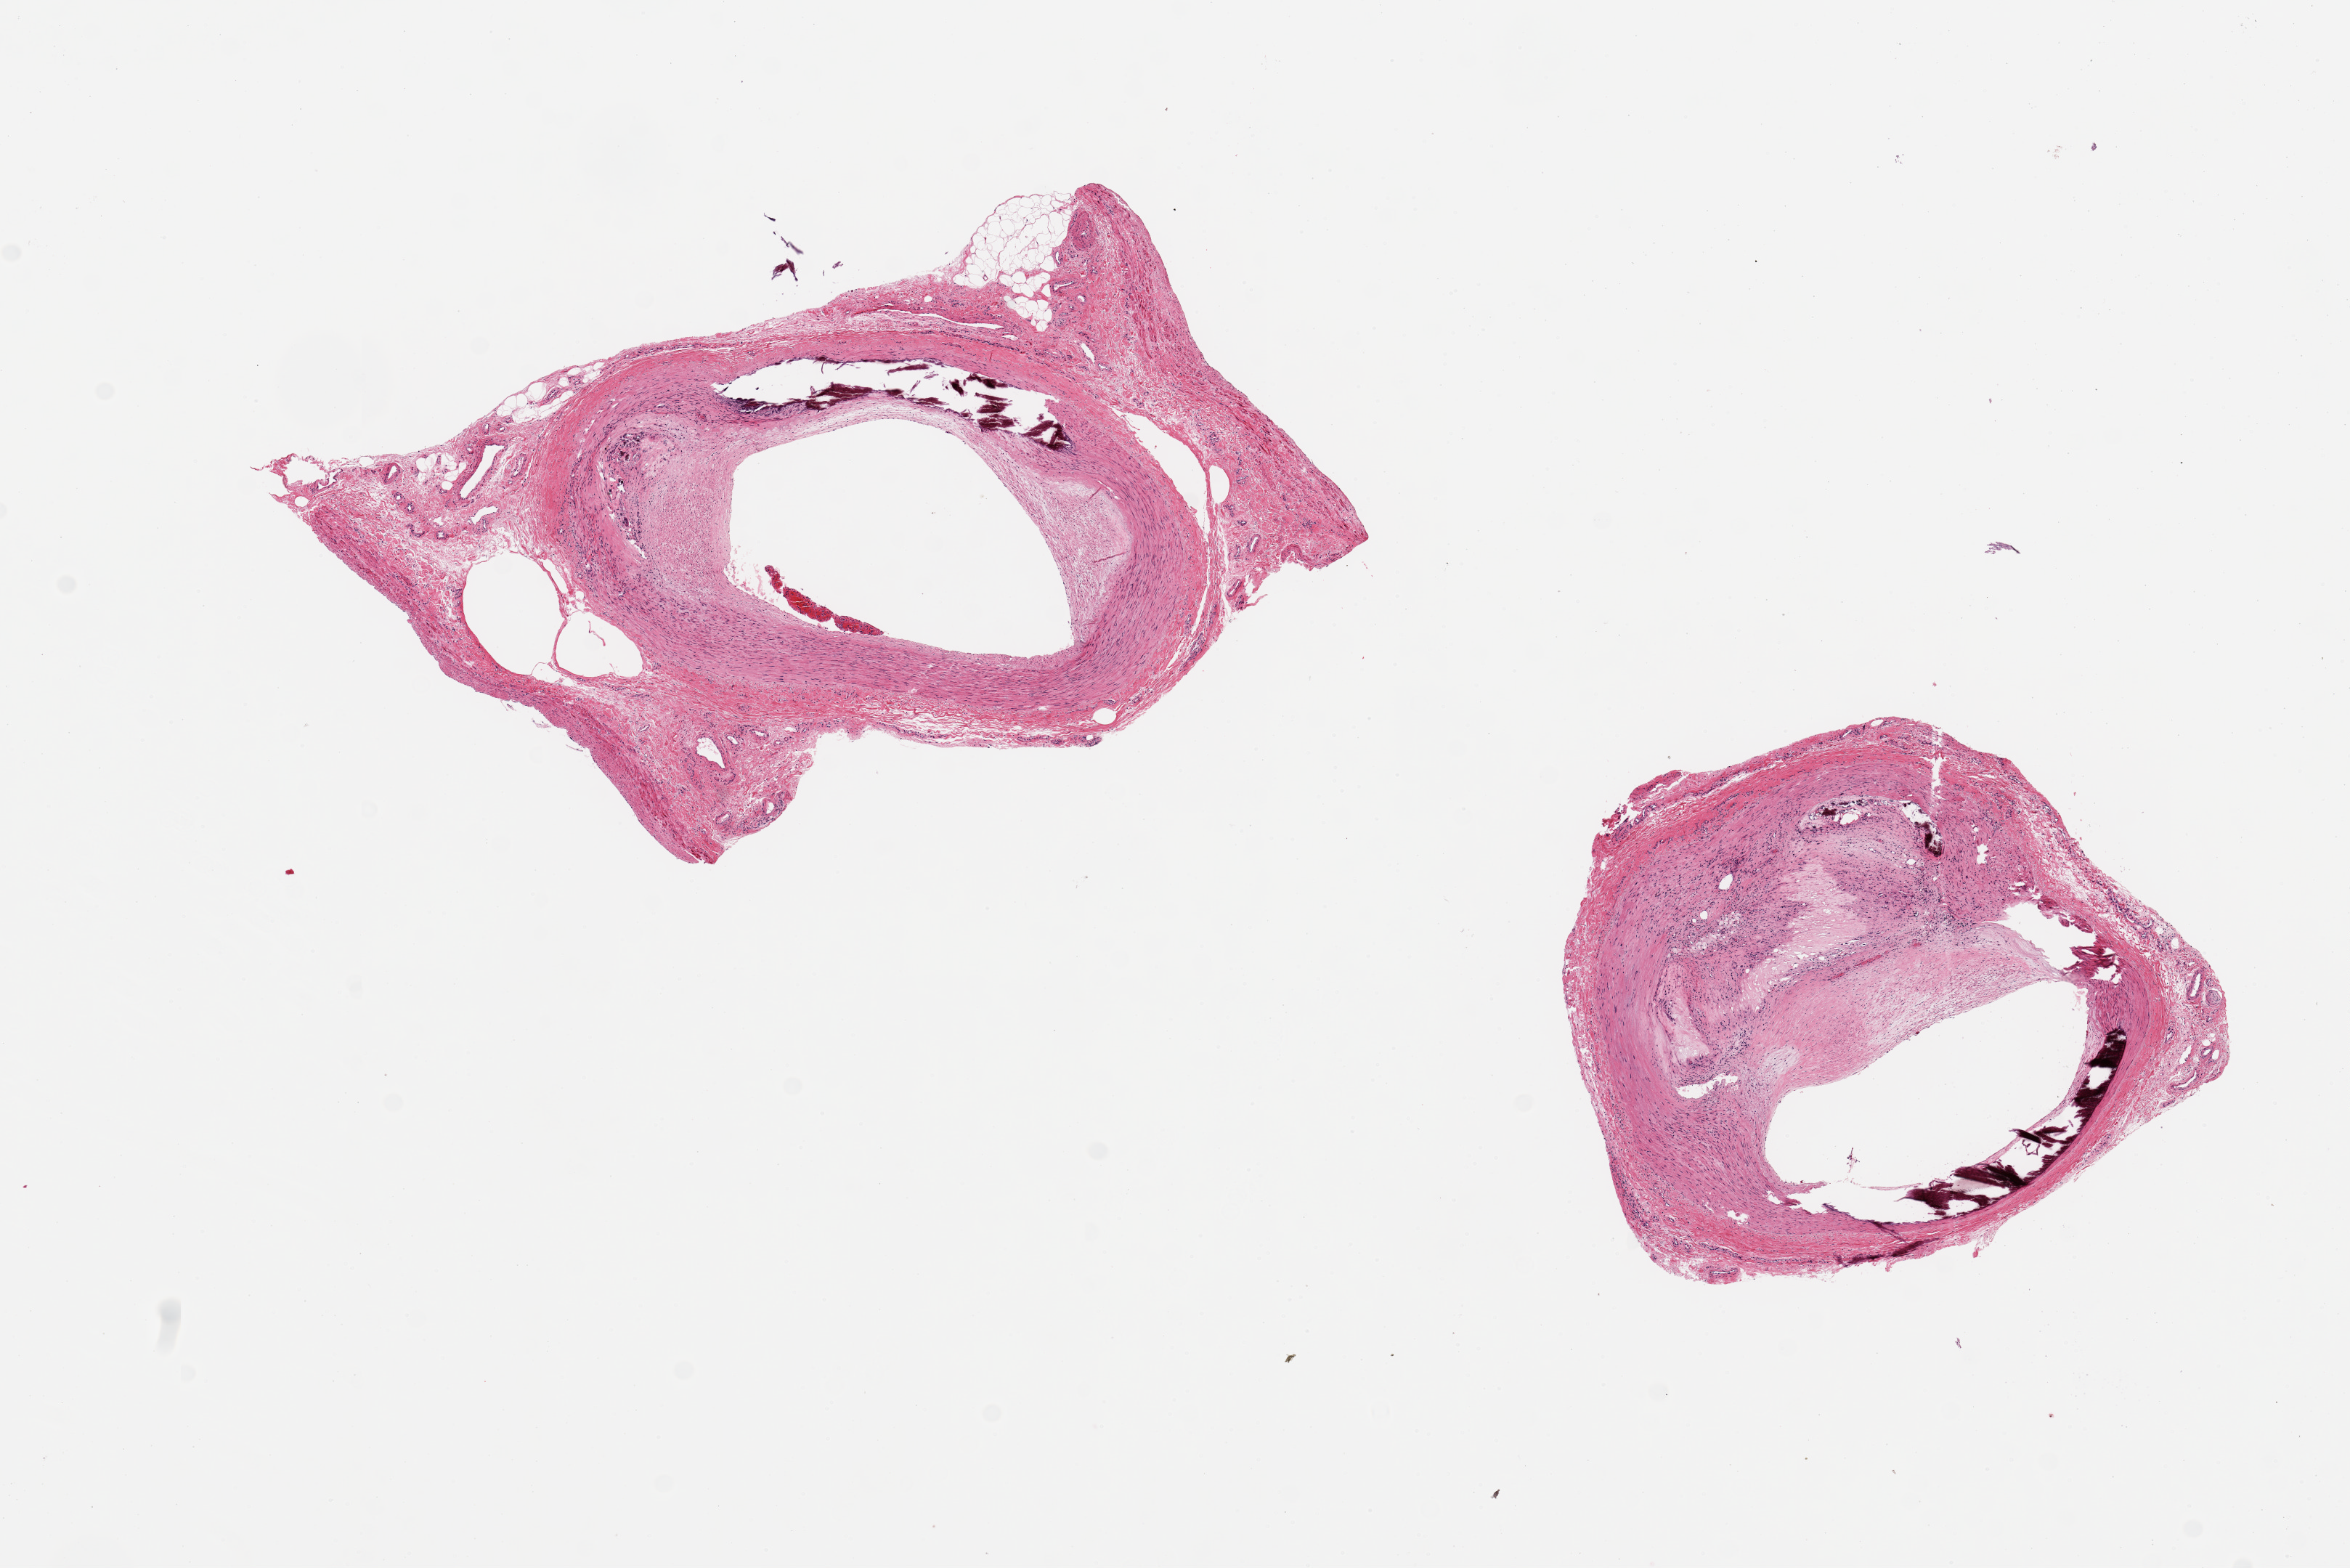
Digitized hematoxylin and eosin (H&E)-stained section — a low-resolution overview of the entire scanned area, about 12.8 x 8.5 mm (slide scanned at 20x). PAXgene-fixed, paraffin-embedded tissue. Sampled site (target tissue): tibial artery. Donor tissue sample. Donor sex: male.
Reviewer comment on this tissue sample: 2 aliquots, ~3mm d. Subtoally occlusive calcified atherosclerosis; also Monckeberg's medial sclerosis.